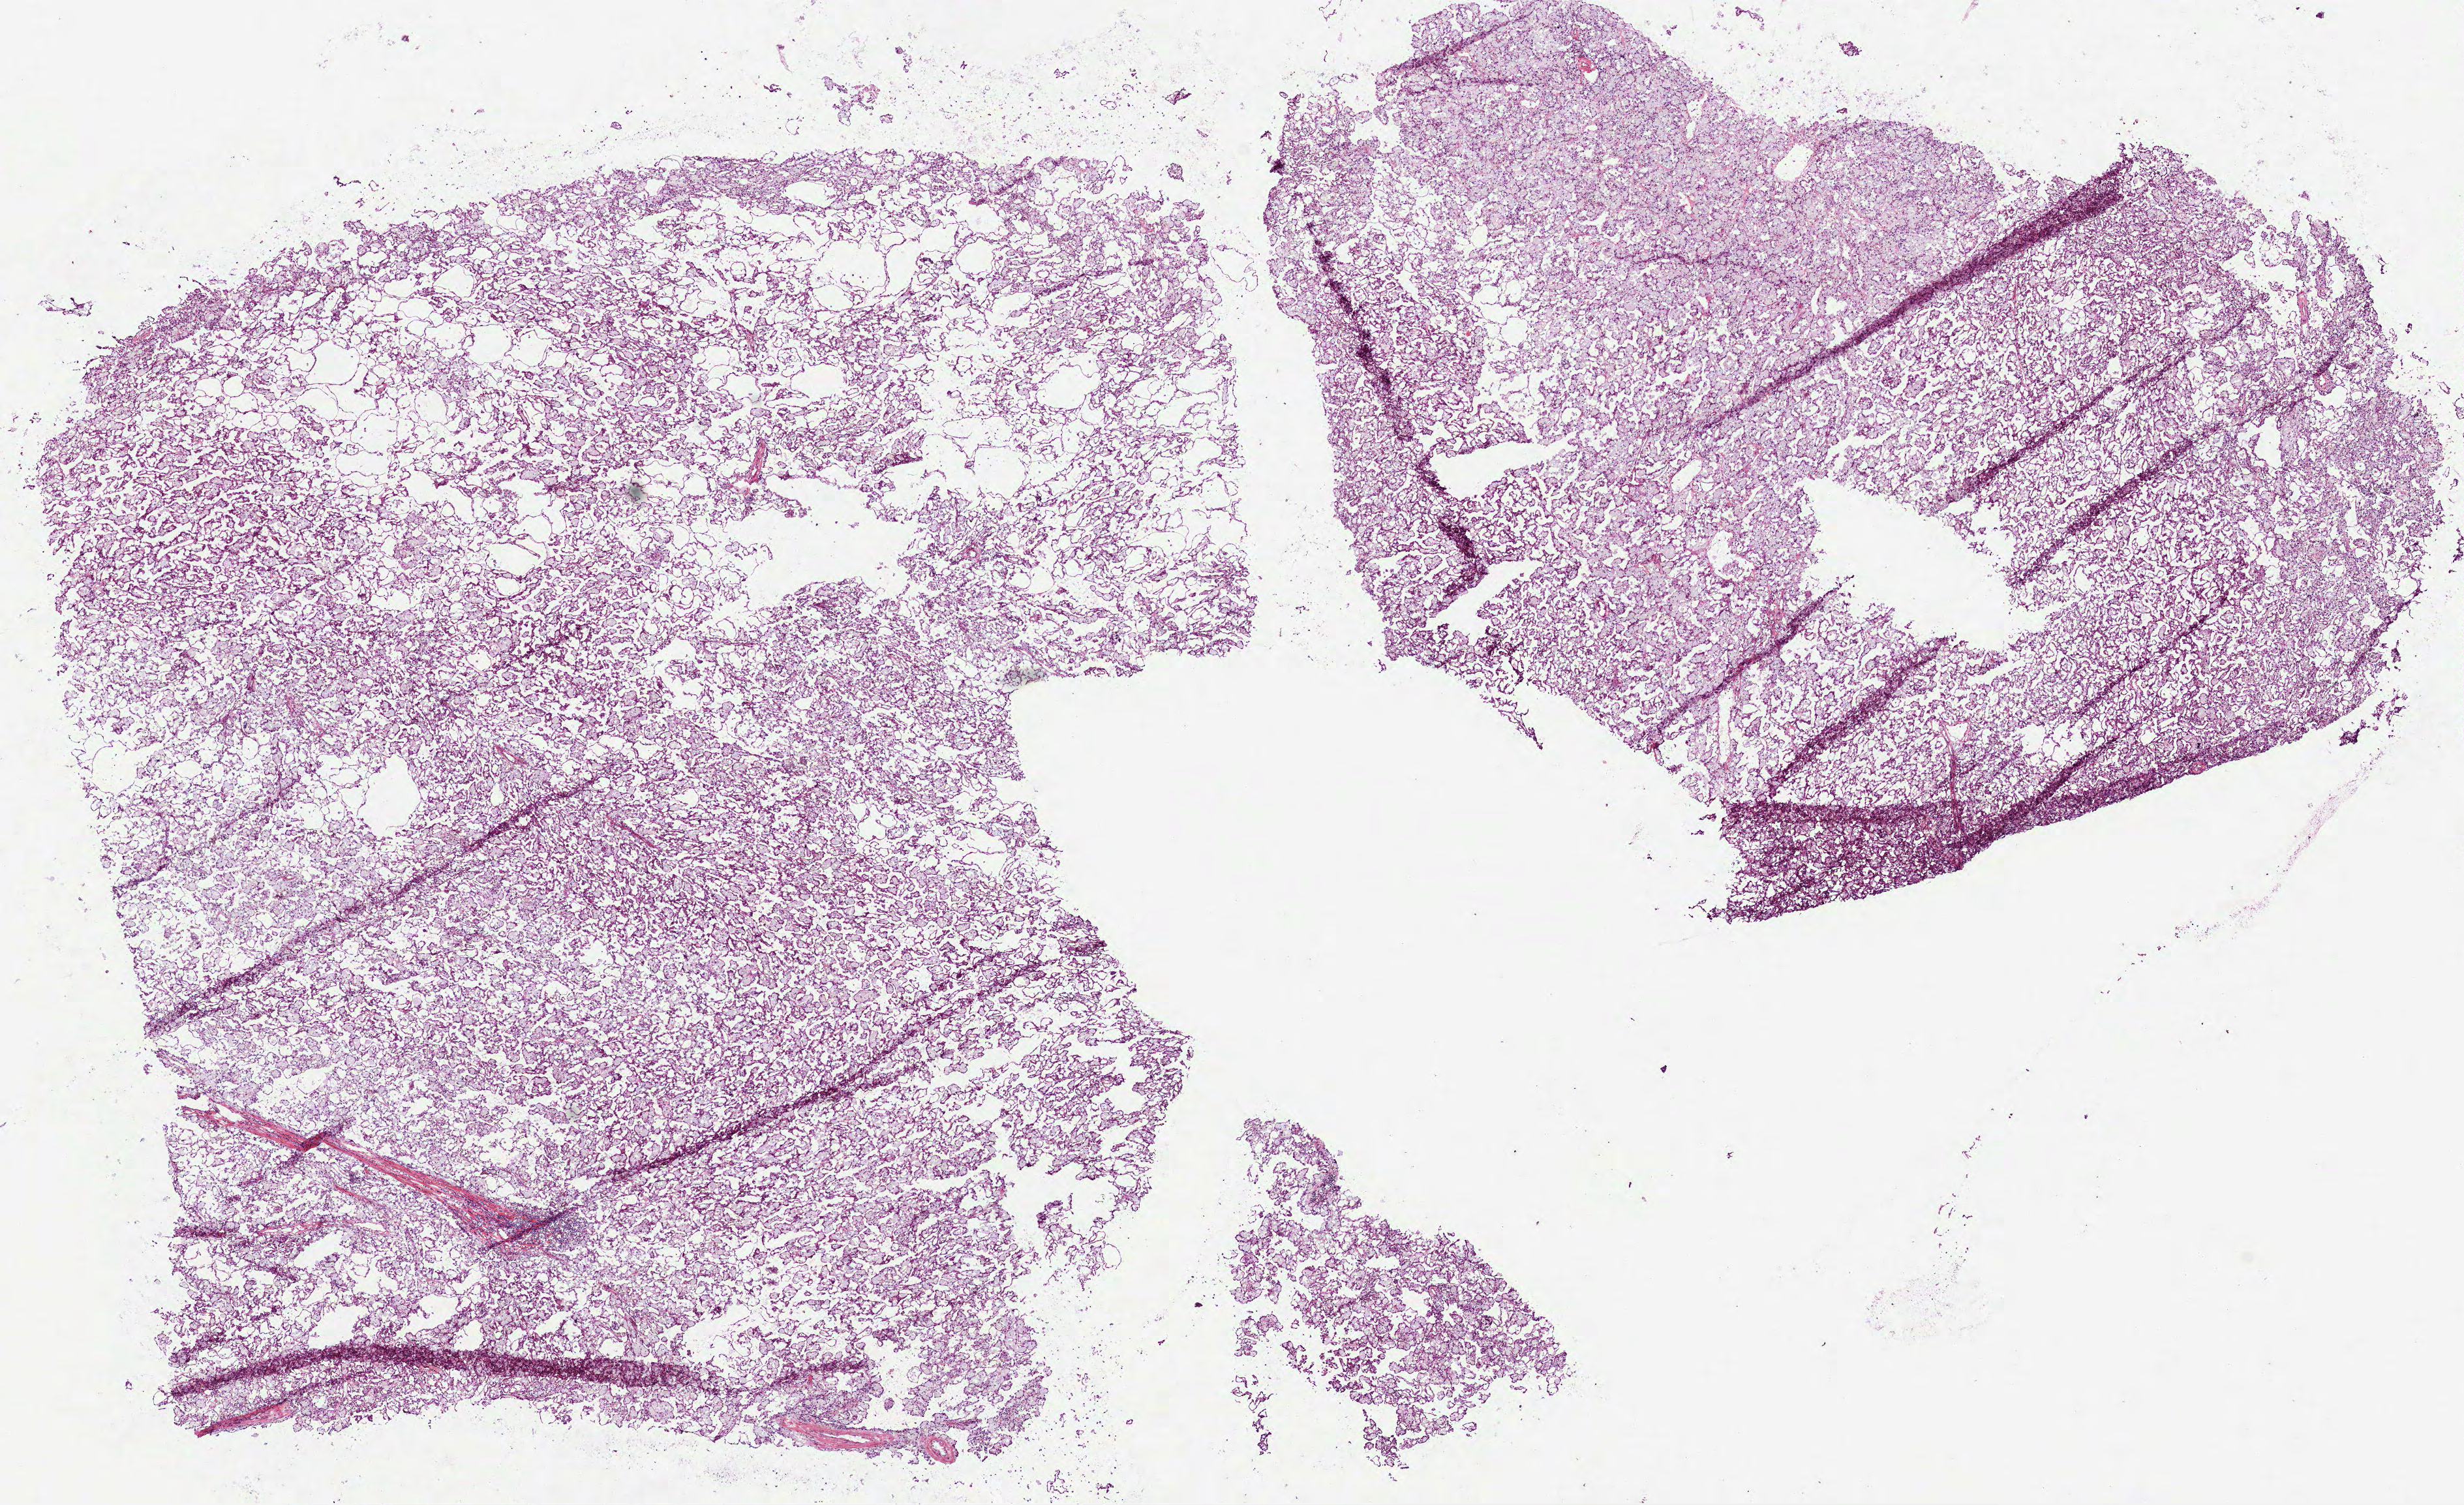
Digitized H&E tissue section (whole slide), a low-resolution overview of the entire scanned area, about 15.2 x 9.3 mm. Frozen section from the bottom of the tissue portion. Sample: primary tumour, kidney. Patient: female, age at initial diagnosis 60 years. Slide review estimates, as recorded: tumour cells 98%, tumour nuclei 85%, normal cells 0%, stromal cells 2%, necrosis 0%. Infiltration values recorded for this section: monocyte infiltration 10%.
- AJCC pathologic stage: II (7th edition)
- histologic diagnosis: Papillary adenocarcinoma, NOS
- laterality: left